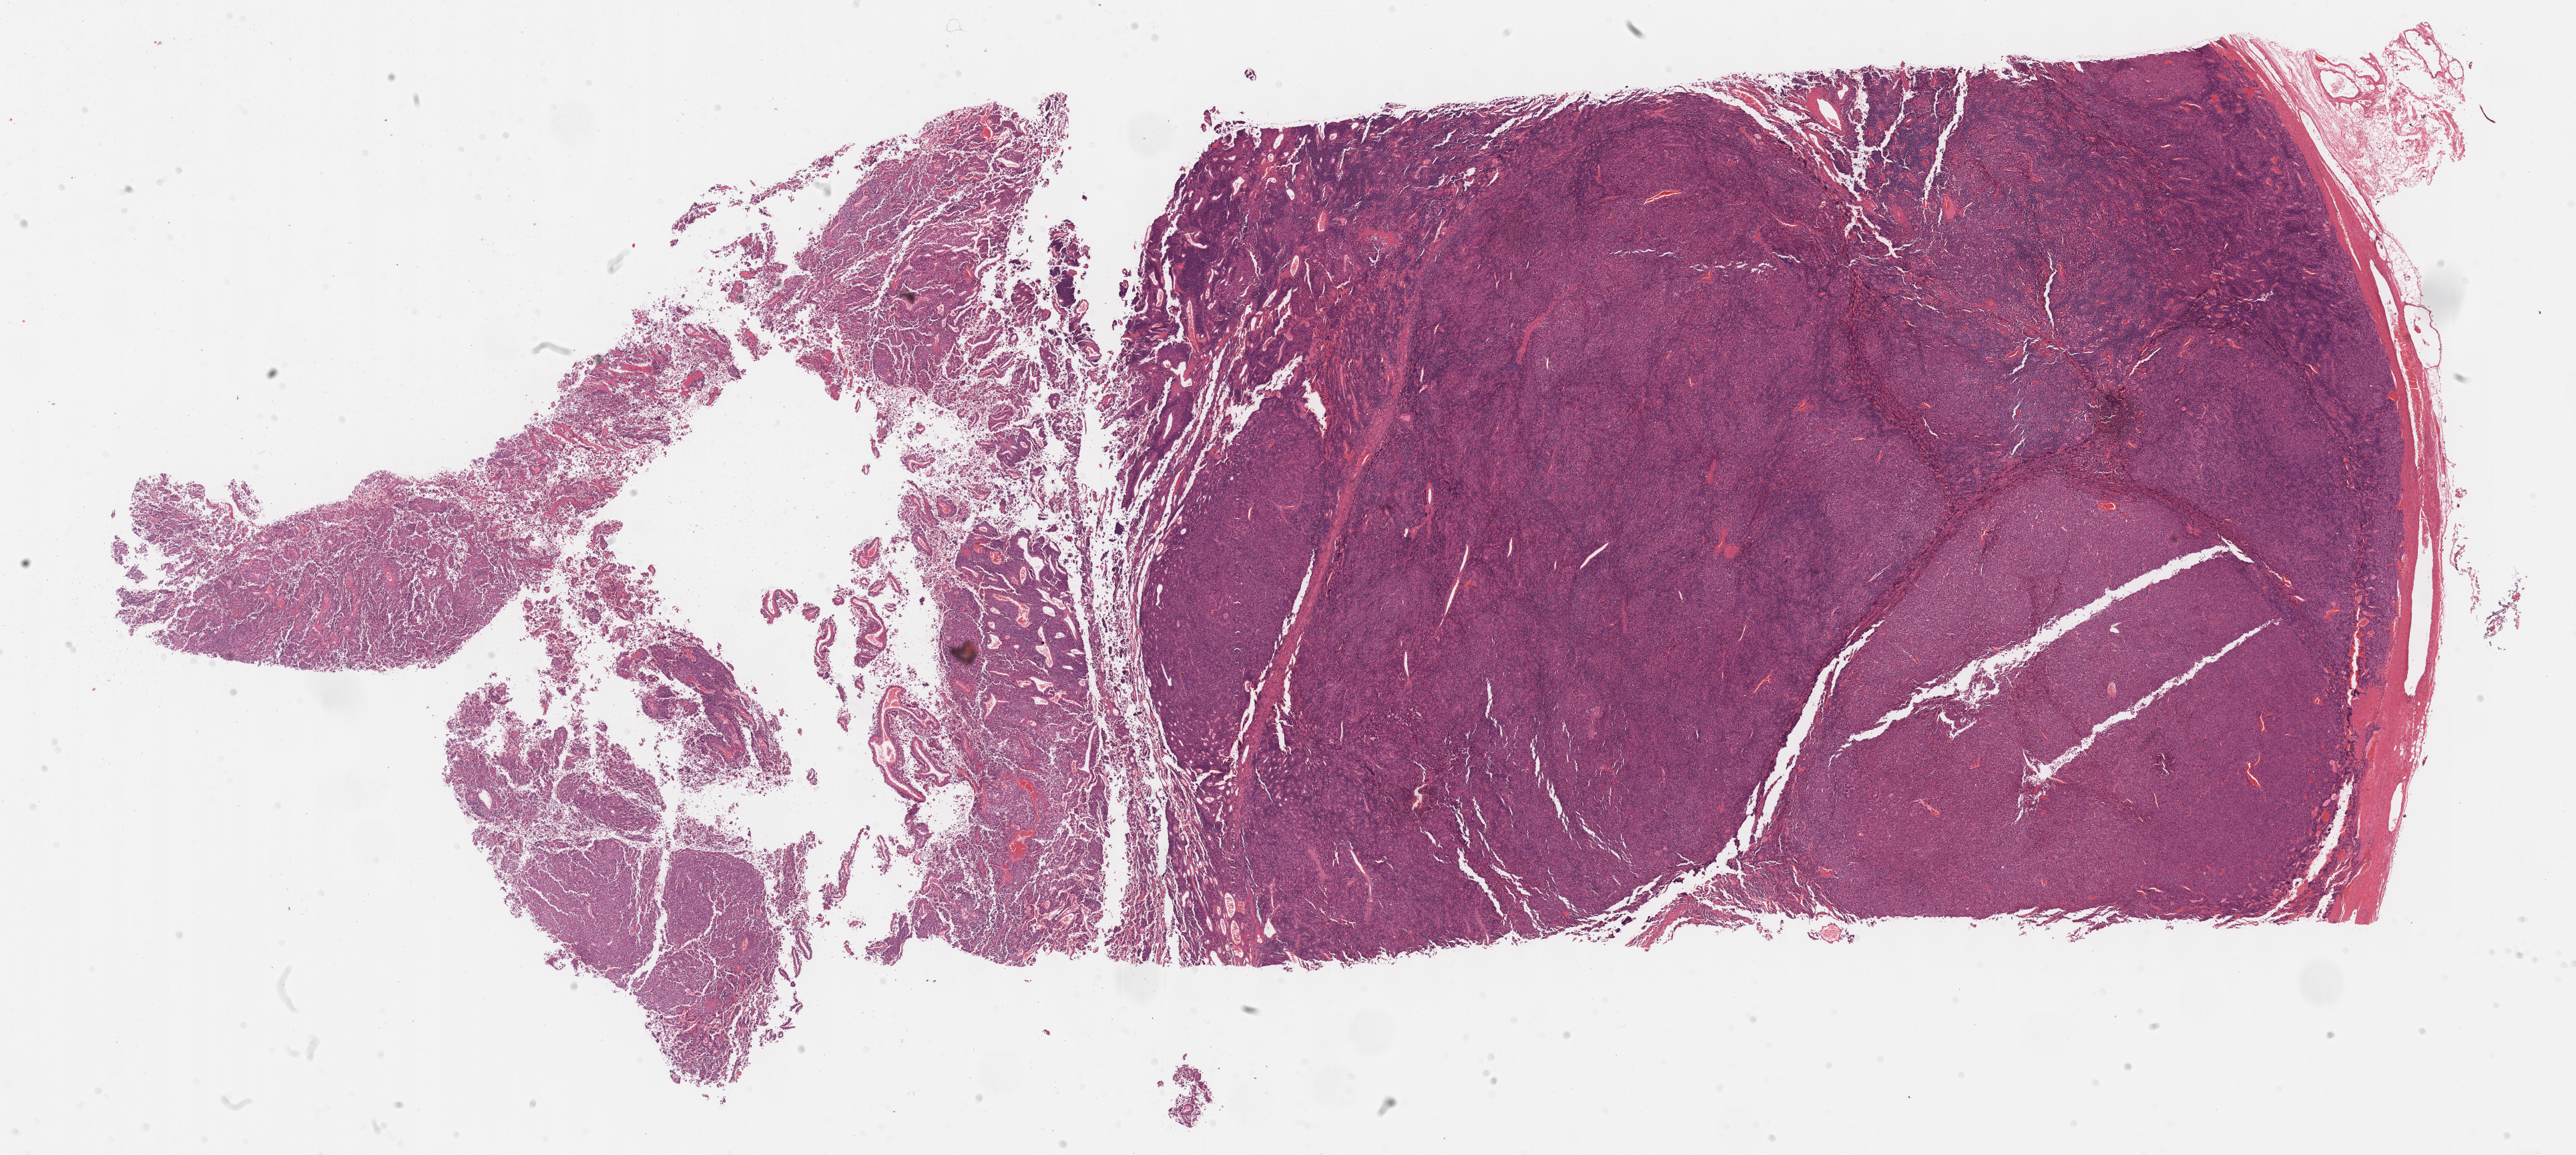
Whole-slide histology image, Hematoxylin and eosin (H&E) stained, whole scanned area (about 31.2 x 14.0 mm, from a 40x scan) shown as a low-resolution overview. Formalin-fixed paraffin-embedded (FFPE) diagnostic section. Adrenal cortex, primary tumour sample. Male, age 58 years at initial diagnosis.
- laterality: left
- diagnosis: Adrenal cortical carcinoma (cortex of adrenal gland)